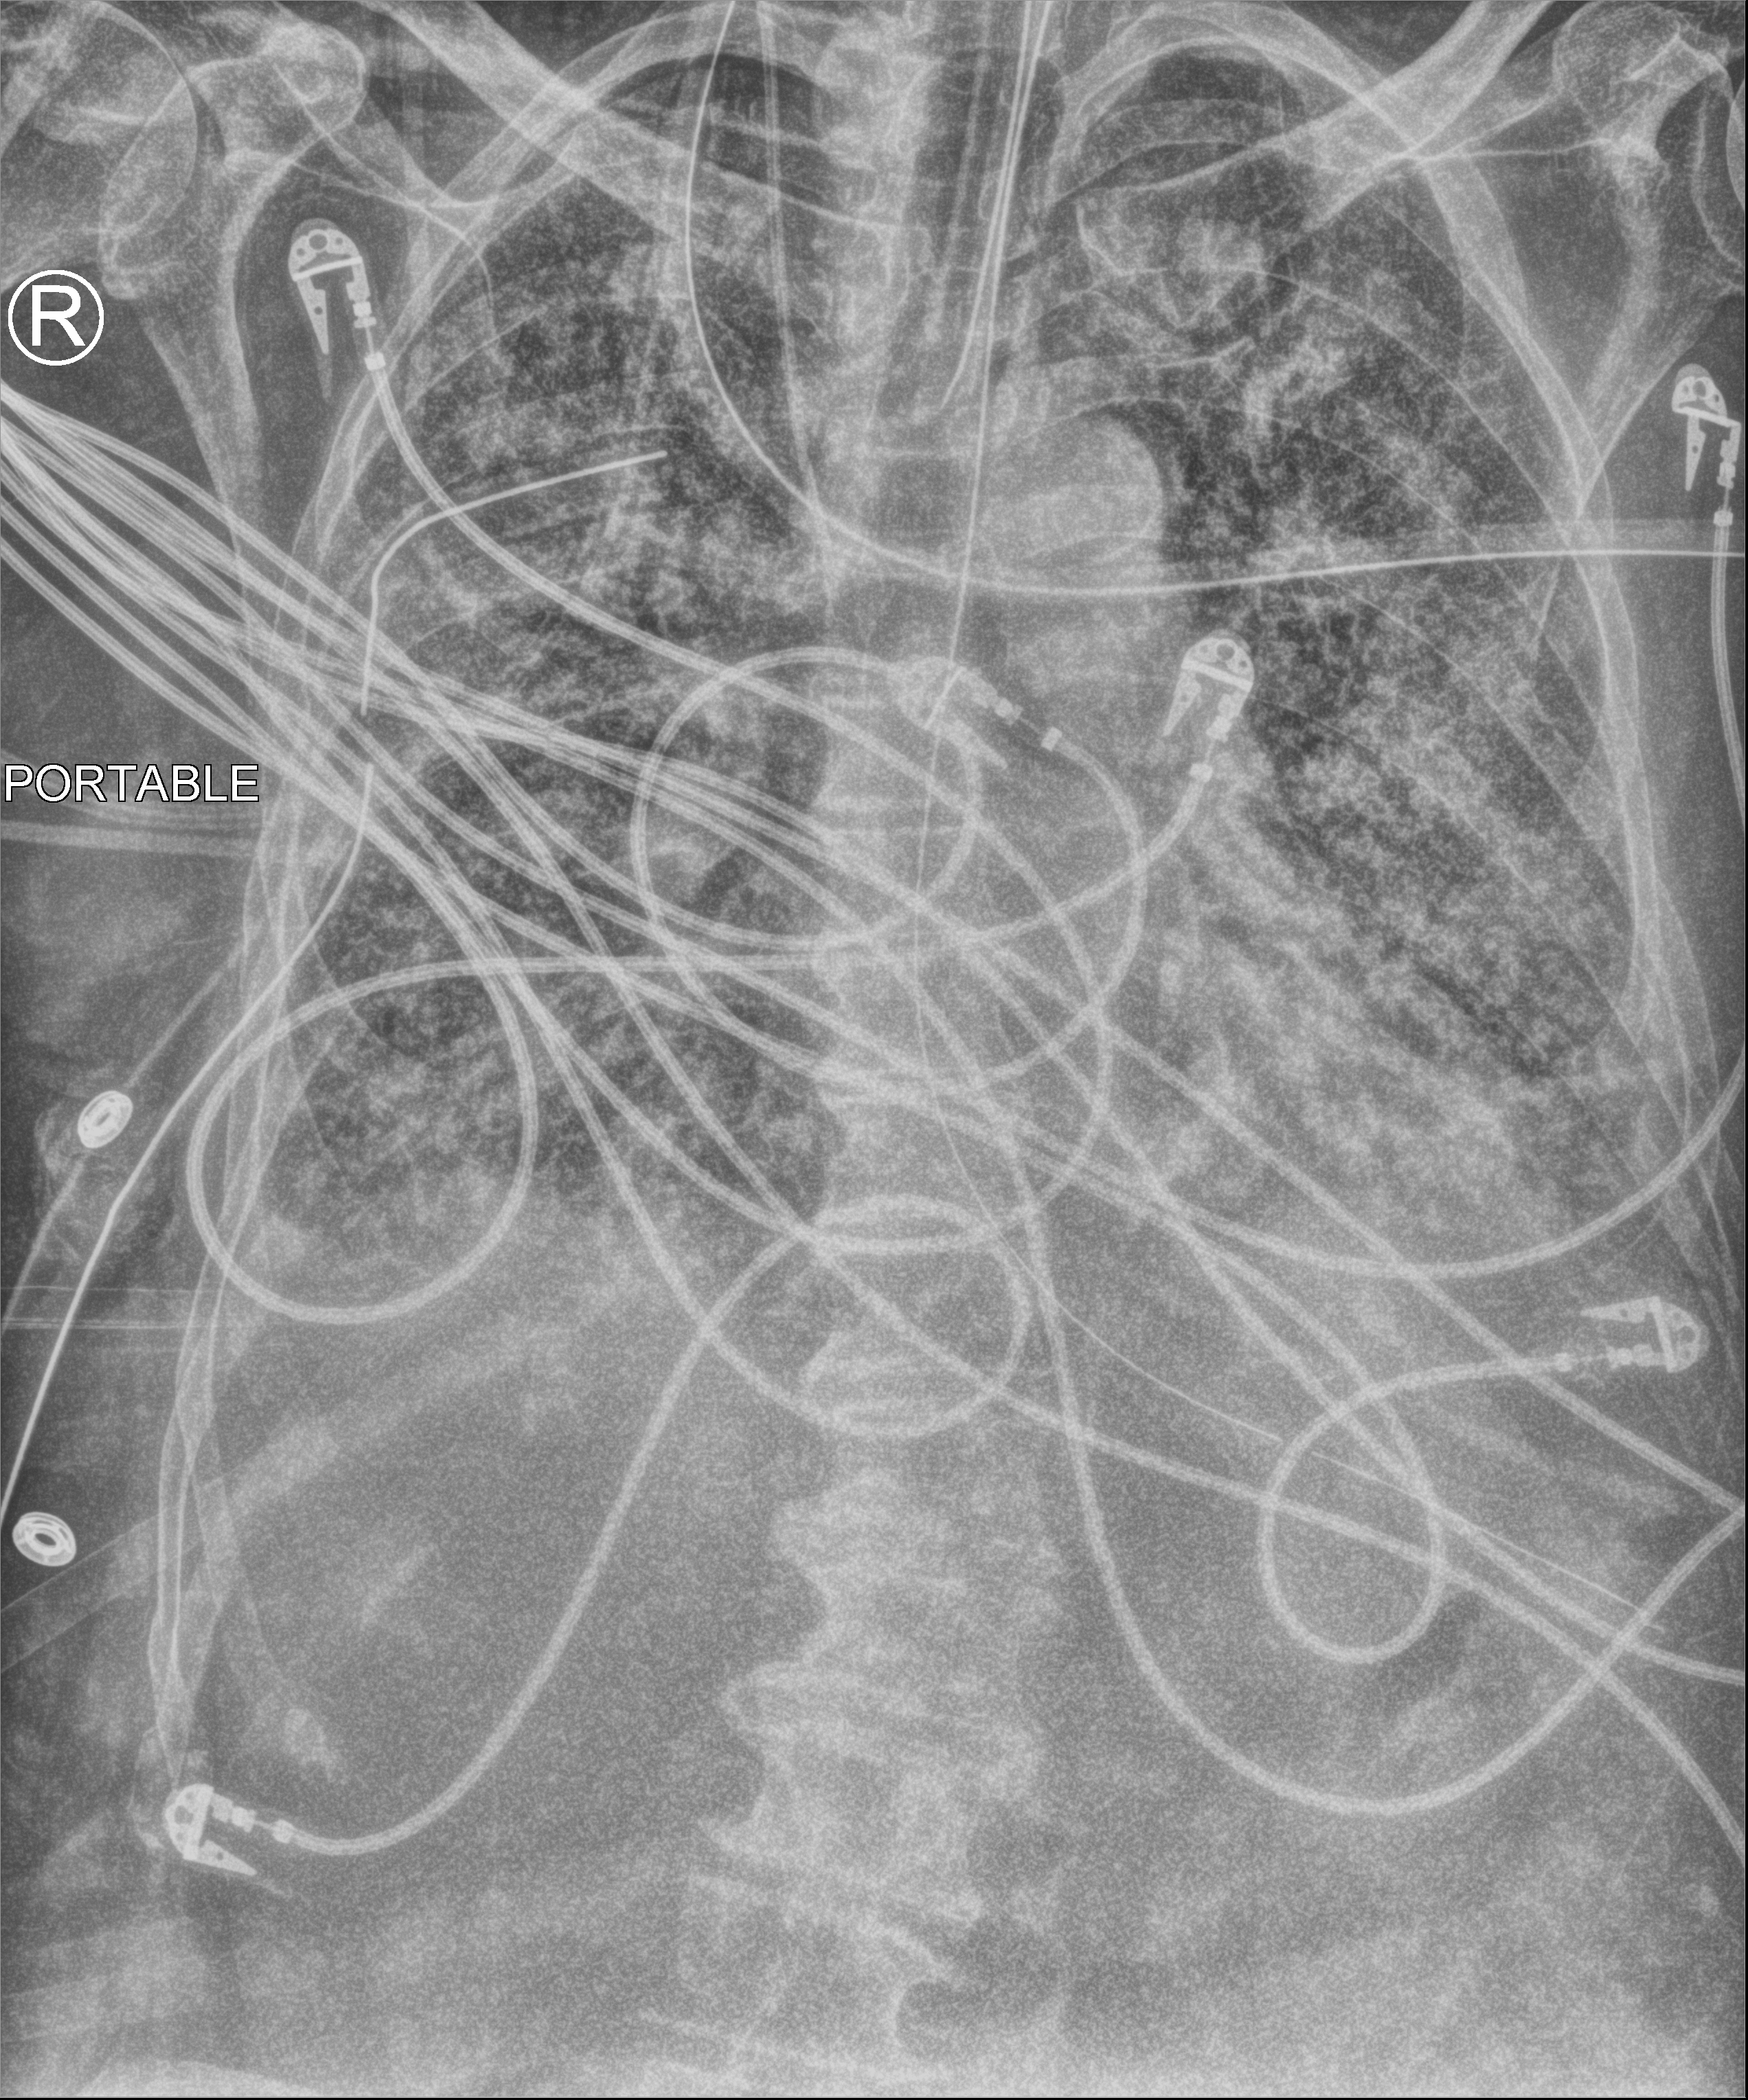
Bedside chest radiograph (computed radiography), anteroposterior (AP) projection. Male patient hospitalised with COVID-19, age 75–90 years.
Hospital-stay facts (about this admission, not read from this image; timing relative to this image not recorded):
- hypertension (admission record): no
- mechanically ventilated during this hospital stay: yes